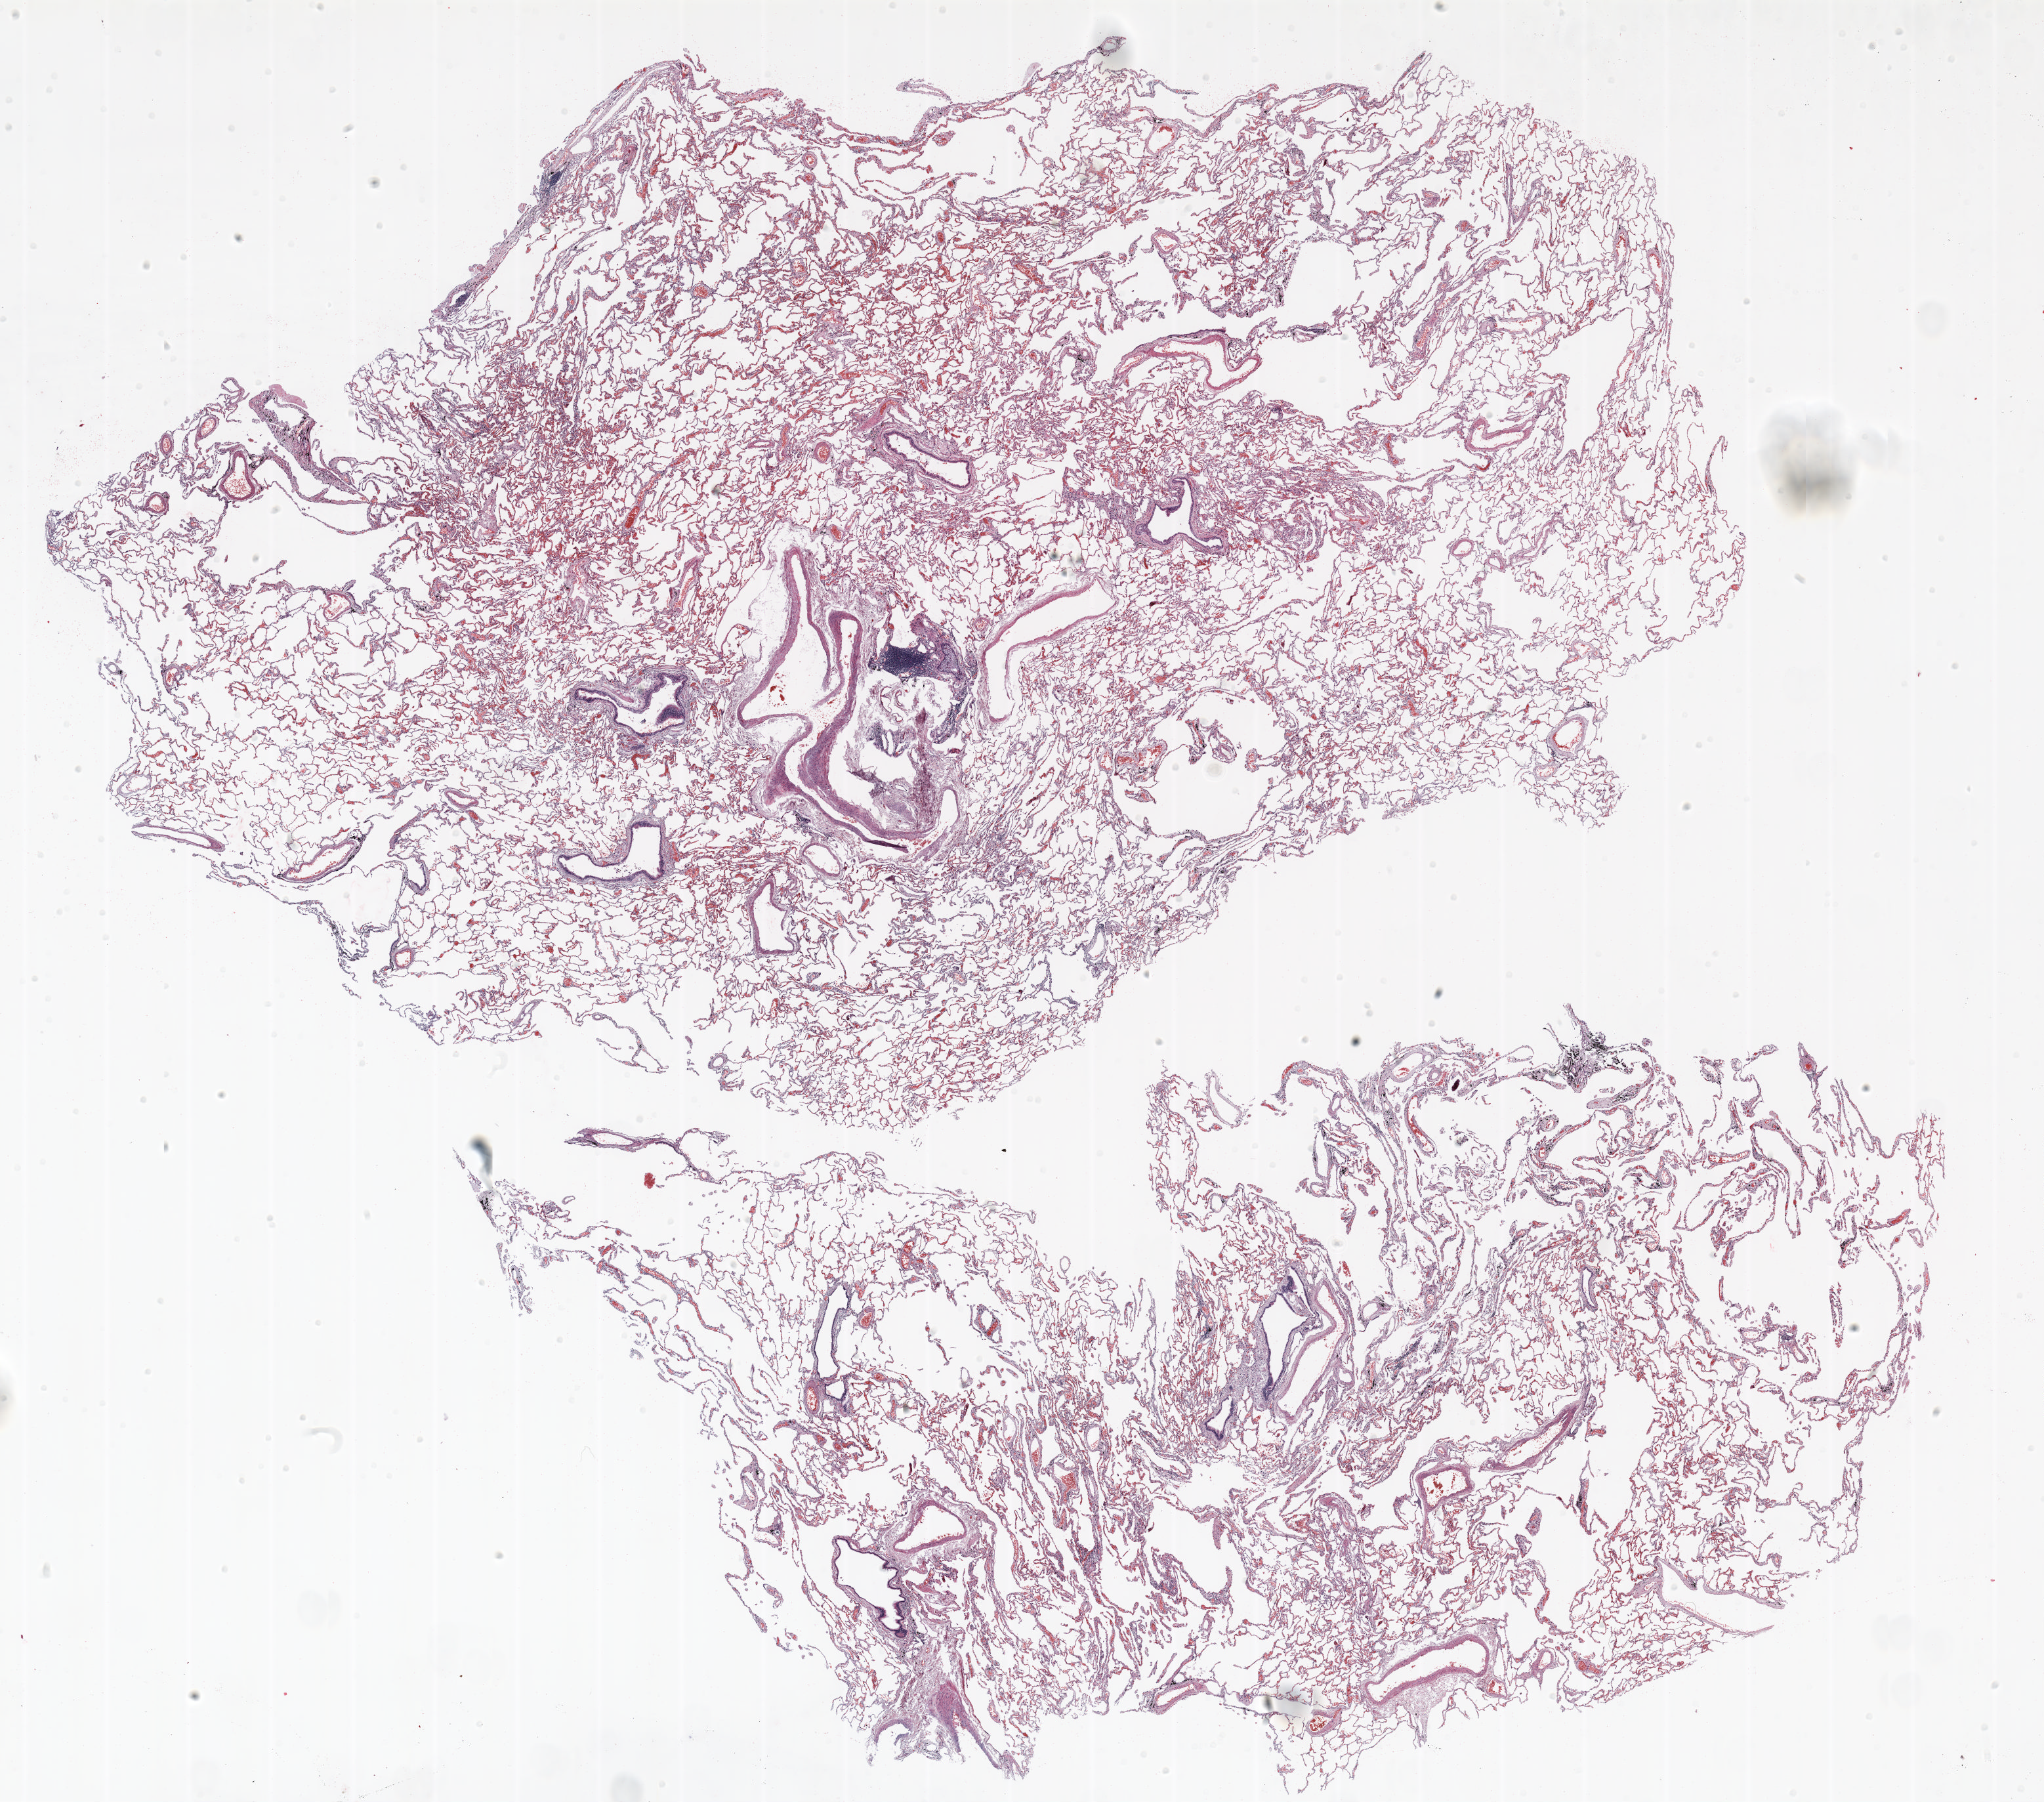
Whole-slide histology image, H&E — low-resolution overview of the scanned area, about 25.0 x 22.1 mm. Formalin-fixed paraffin-embedded (FFPE) section. Lung. Male patient, aged 62 at enrolment. Former smoker at enrolment.
Participant's lung-cancer diagnosis: Adenocarcinoma, NOS (ICD-O-3 8140/3).